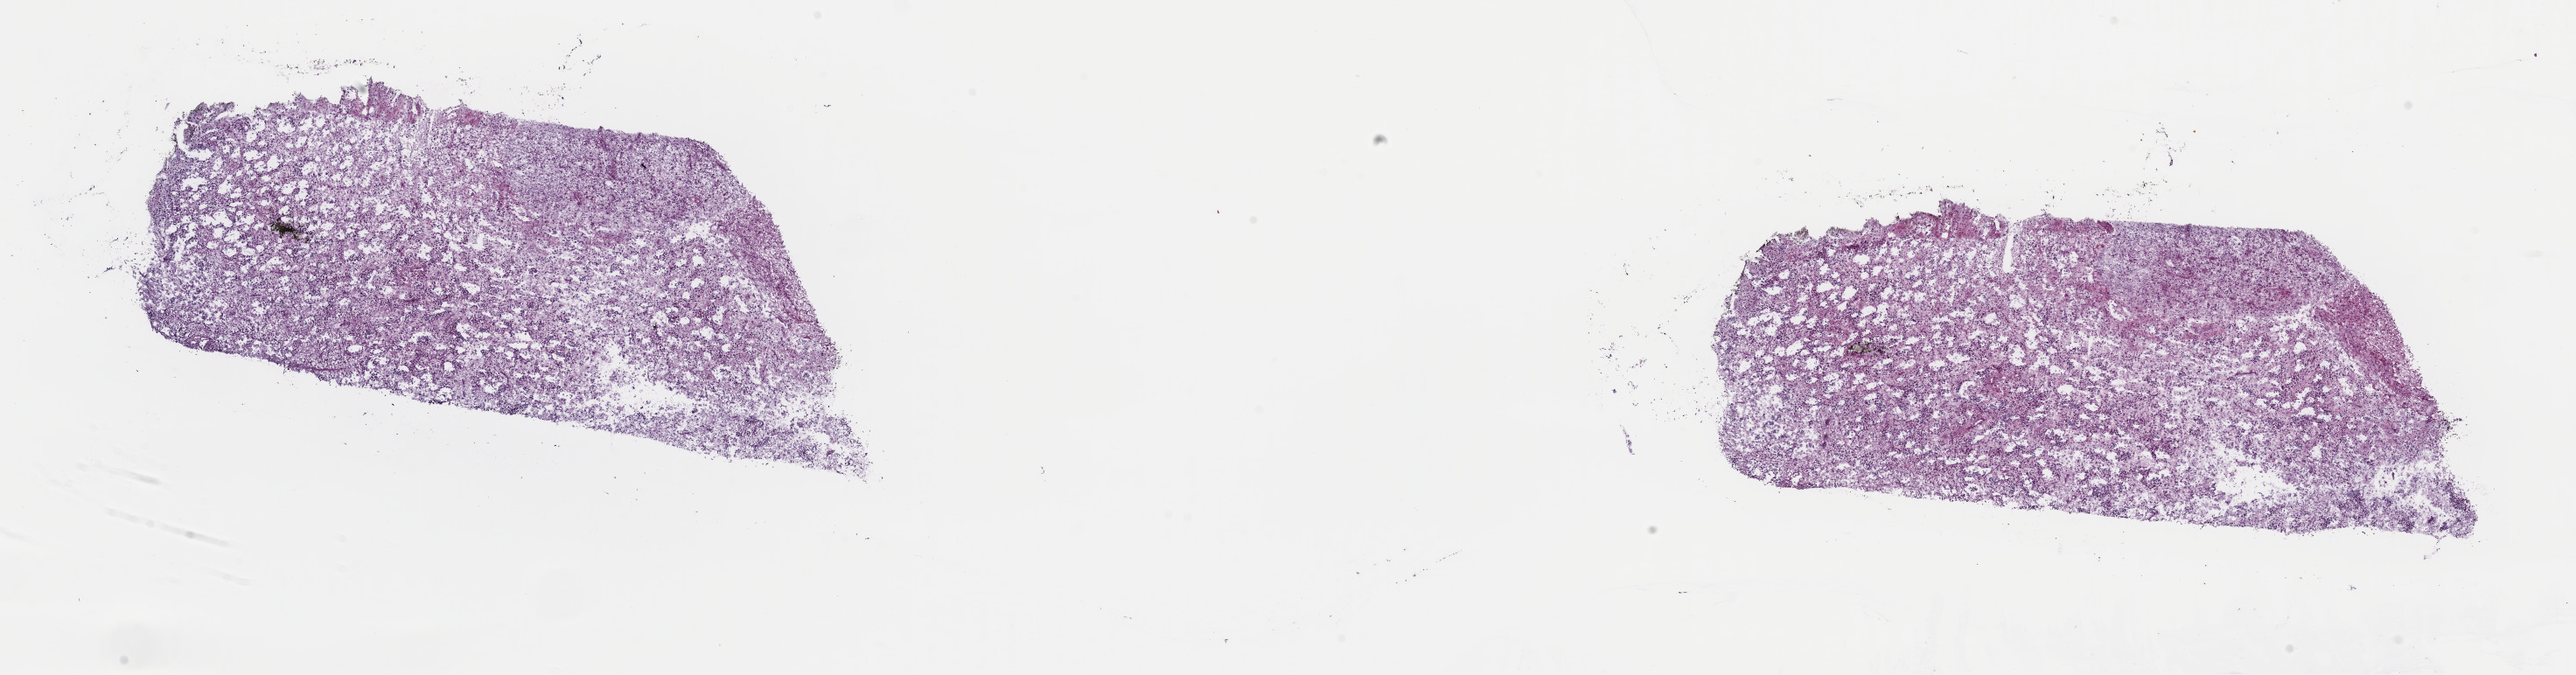
Digitized Hematoxylin and eosin (H&E) stained tissue section (whole slide) — shown as a low-resolution overview of the whole scanned area (about 23.3 x 6.1 mm); frozen section from the top of the tissue portion; brain, primary tumour sample. Male, age 35 years at initial diagnosis. Histologic grade: G2 (moderately differentiated). Pathologist review of this section (percent, as recorded): tumour cells 75%, tumour nuclei 90%, normal cells 10%, stromal cells 15%, necrosis 0%. Infiltration values recorded for this section: lymphocyte infiltration 0%, monocyte infiltration 0%, neutrophil infiltration 0%.
- laterality: left
- pathologic diagnosis: Astrocytoma, NOS